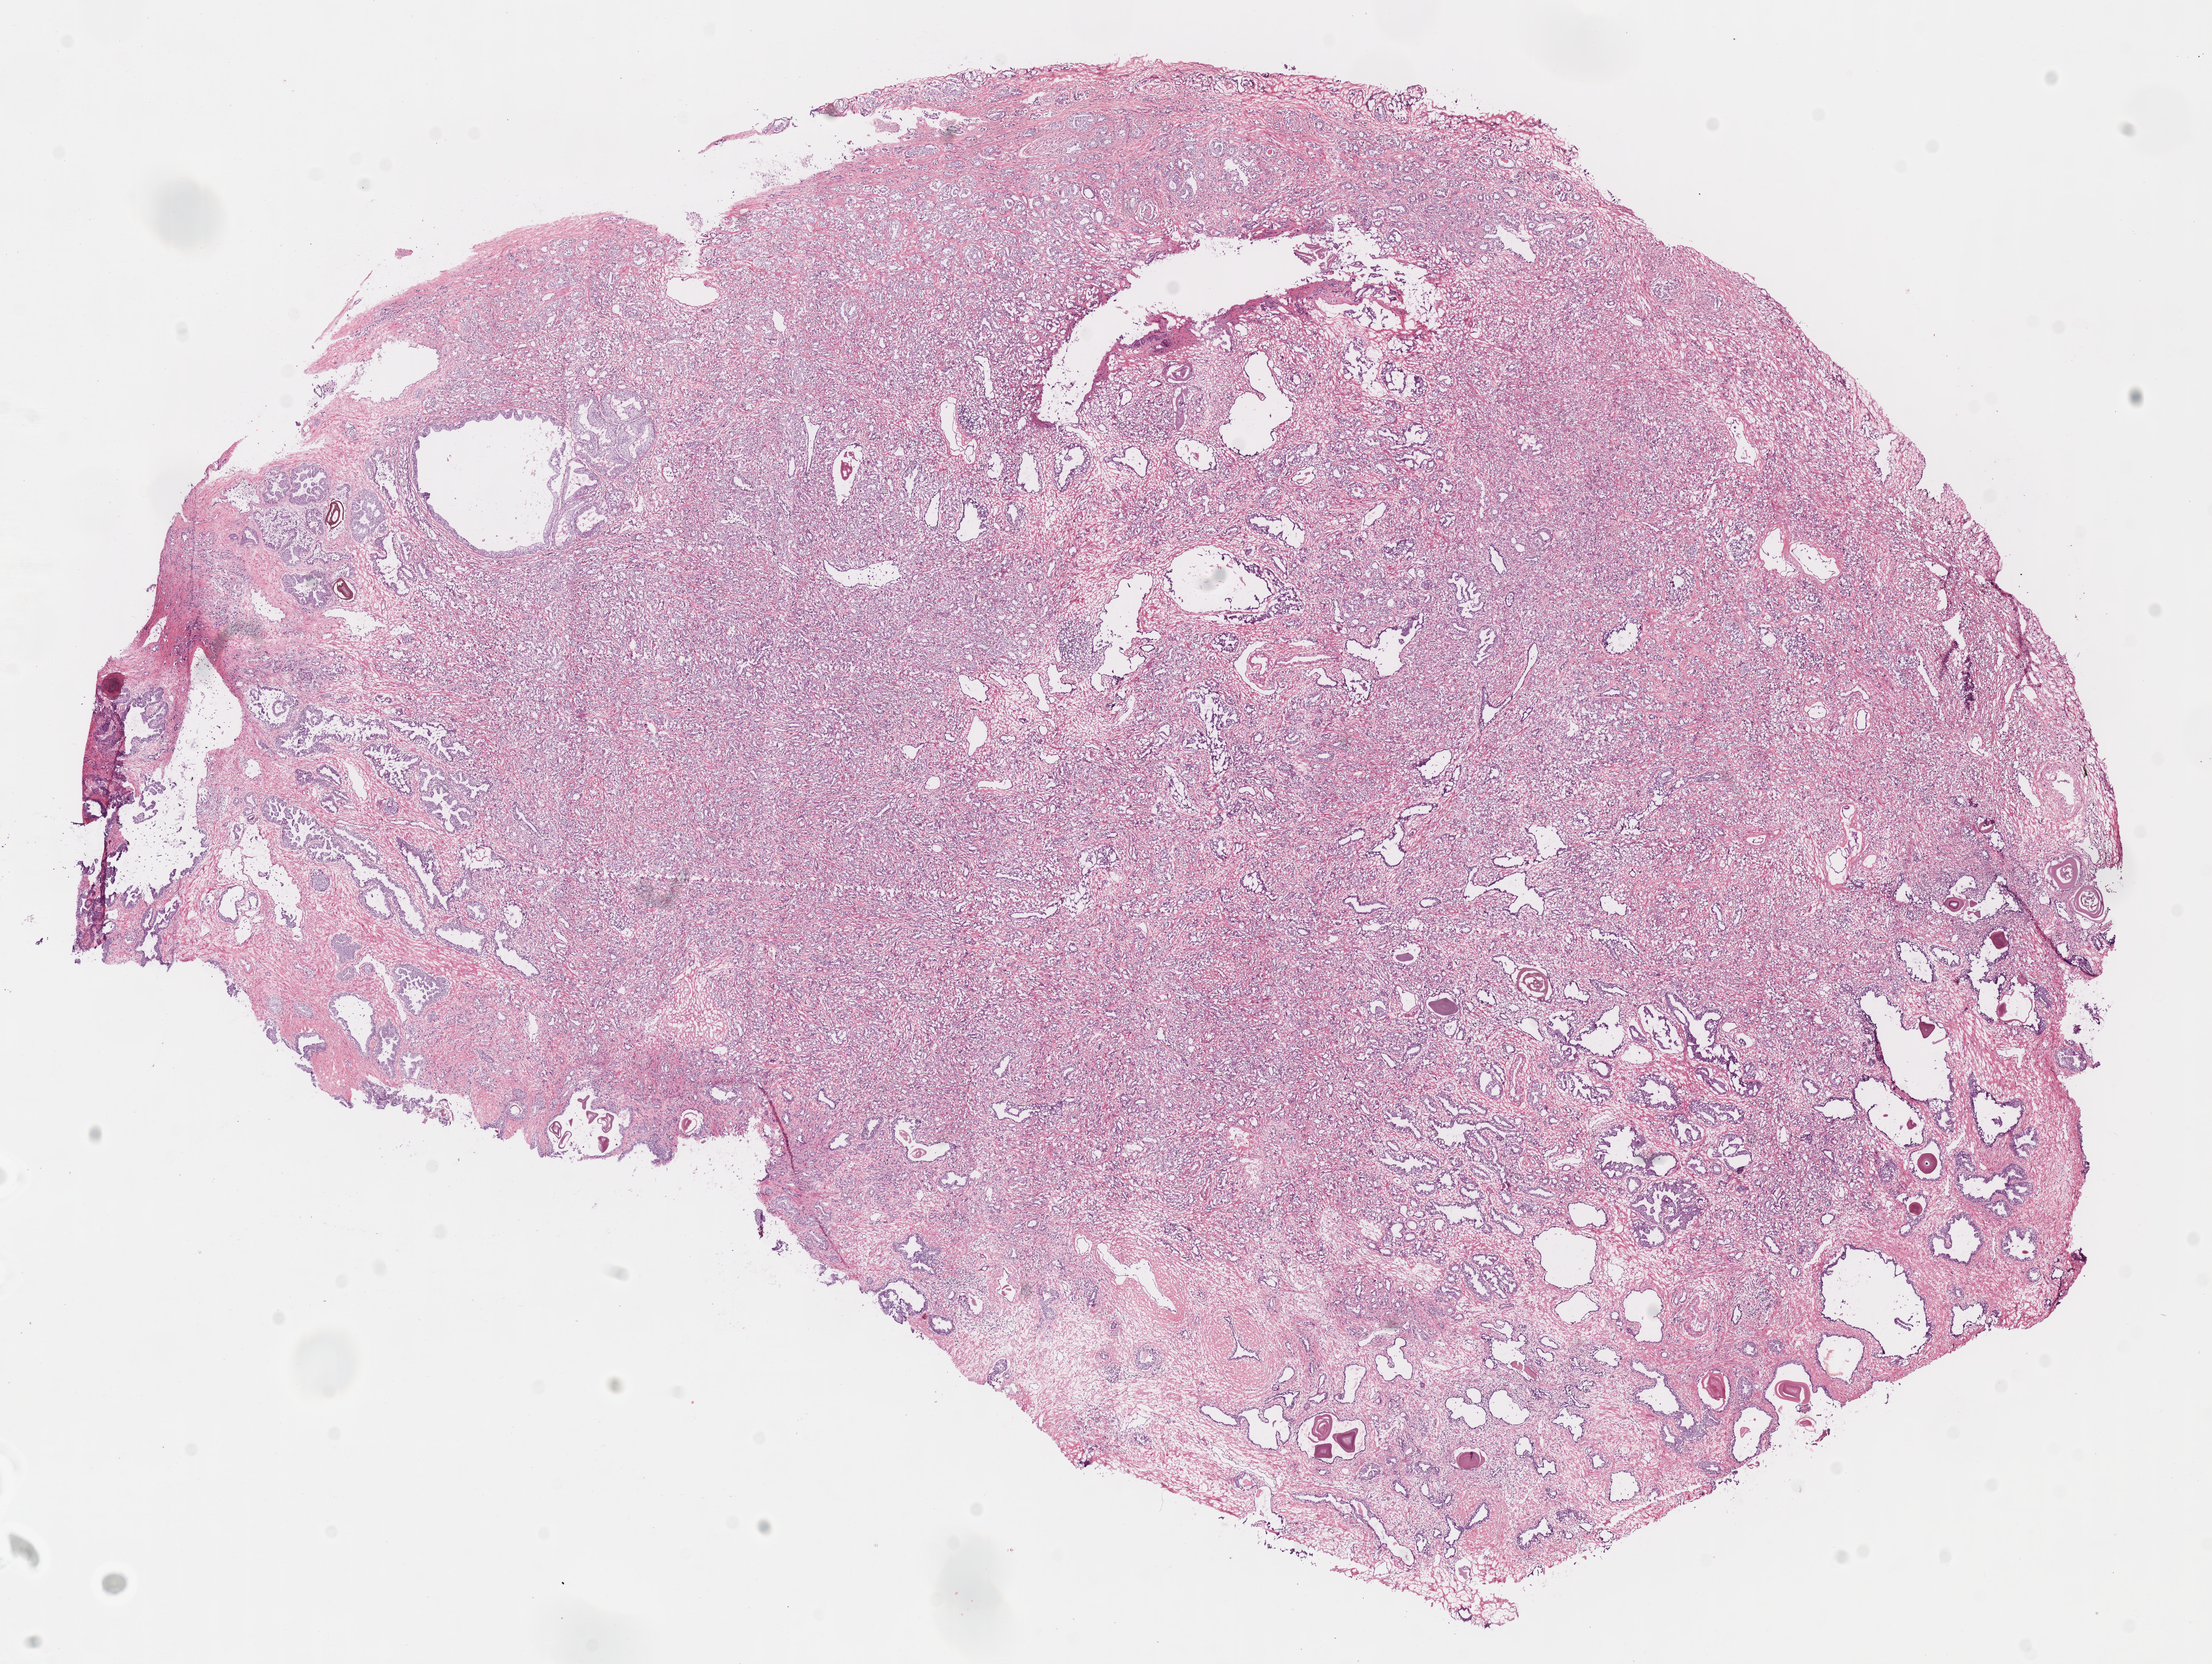
Hematoxylin and eosin (H&E) stained whole-slide image — whole scanned area (about 15.2 x 11.5 mm, acquisition: 40x scan) shown as a low-resolution overview; frozen section from the top of the tissue portion; sample: primary tumour, prostate. Male, age 66 years at initial diagnosis. Gleason score: 8 (4+4). Composition of this section per pathologist review: tumour cells 70%, tumour nuclei 70%, normal cells 15%, stromal cells 15%, necrosis 0%.
Laterality: bilateral. Pathologic diagnosis: Acinar cell carcinoma (prostate gland). Lymph nodes positive (case pathology): 0 of 10 examined.